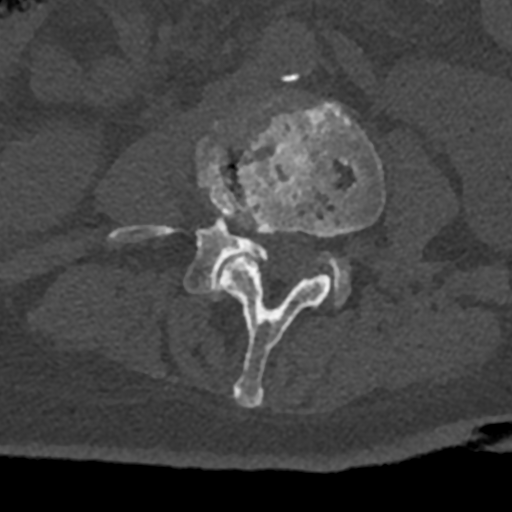
CT including the spine, one axial slice; slice 294 of 797 in the series (ordered by position); reconstruction kernel Br40s/3; 120 kVp; bone window (W 1800 / L 400 HU); 0.5 mm slice thickness; 512 × 512 image matrix. Male patient, age 74 years. From the clinical record (not read from this slice): primary cancer: renal; vertebrae with lytic lesions (as recorded): T10, L1, L2, L3, L4, L5.
Outlined on this slice (semi-automatic segmentation, software-assisted and operator-edited):
- L3 vertebra: bounding box <221,101,385,408> (left, top, right, bottom; pixels)
- L4 vertebra: <109,142,349,306>